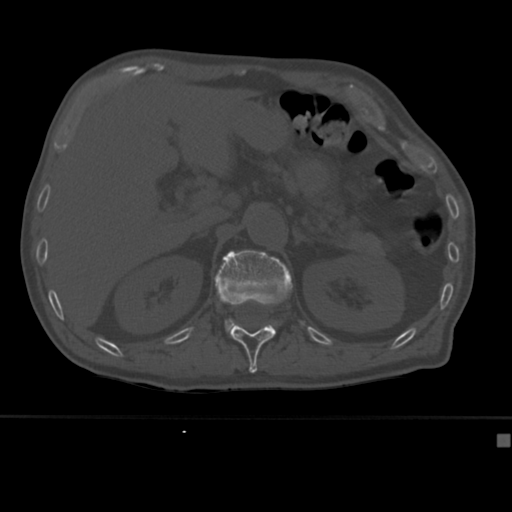
CT including the spine, one axial slice; slice 182 of 430 in the series (ordered by position); reconstruction kernel Br40s; 120 kVp; bone window (W 1800 / L 400 HU); 1.5 mm slice thickness; 512 × 512 image matrix, field of view 337 × 337 mm. Male patient, age 64 years. Case-level facts recorded for this patient, not image findings: primary cancer: uterus.
Annotated regions visible in this slice (semi-automatically segmented with operator editing):
- L1 vertebra: box from (x=214, y=250) to (x=293, y=337) px
- T12 vertebra: (x=231, y=325)–(x=276, y=373)